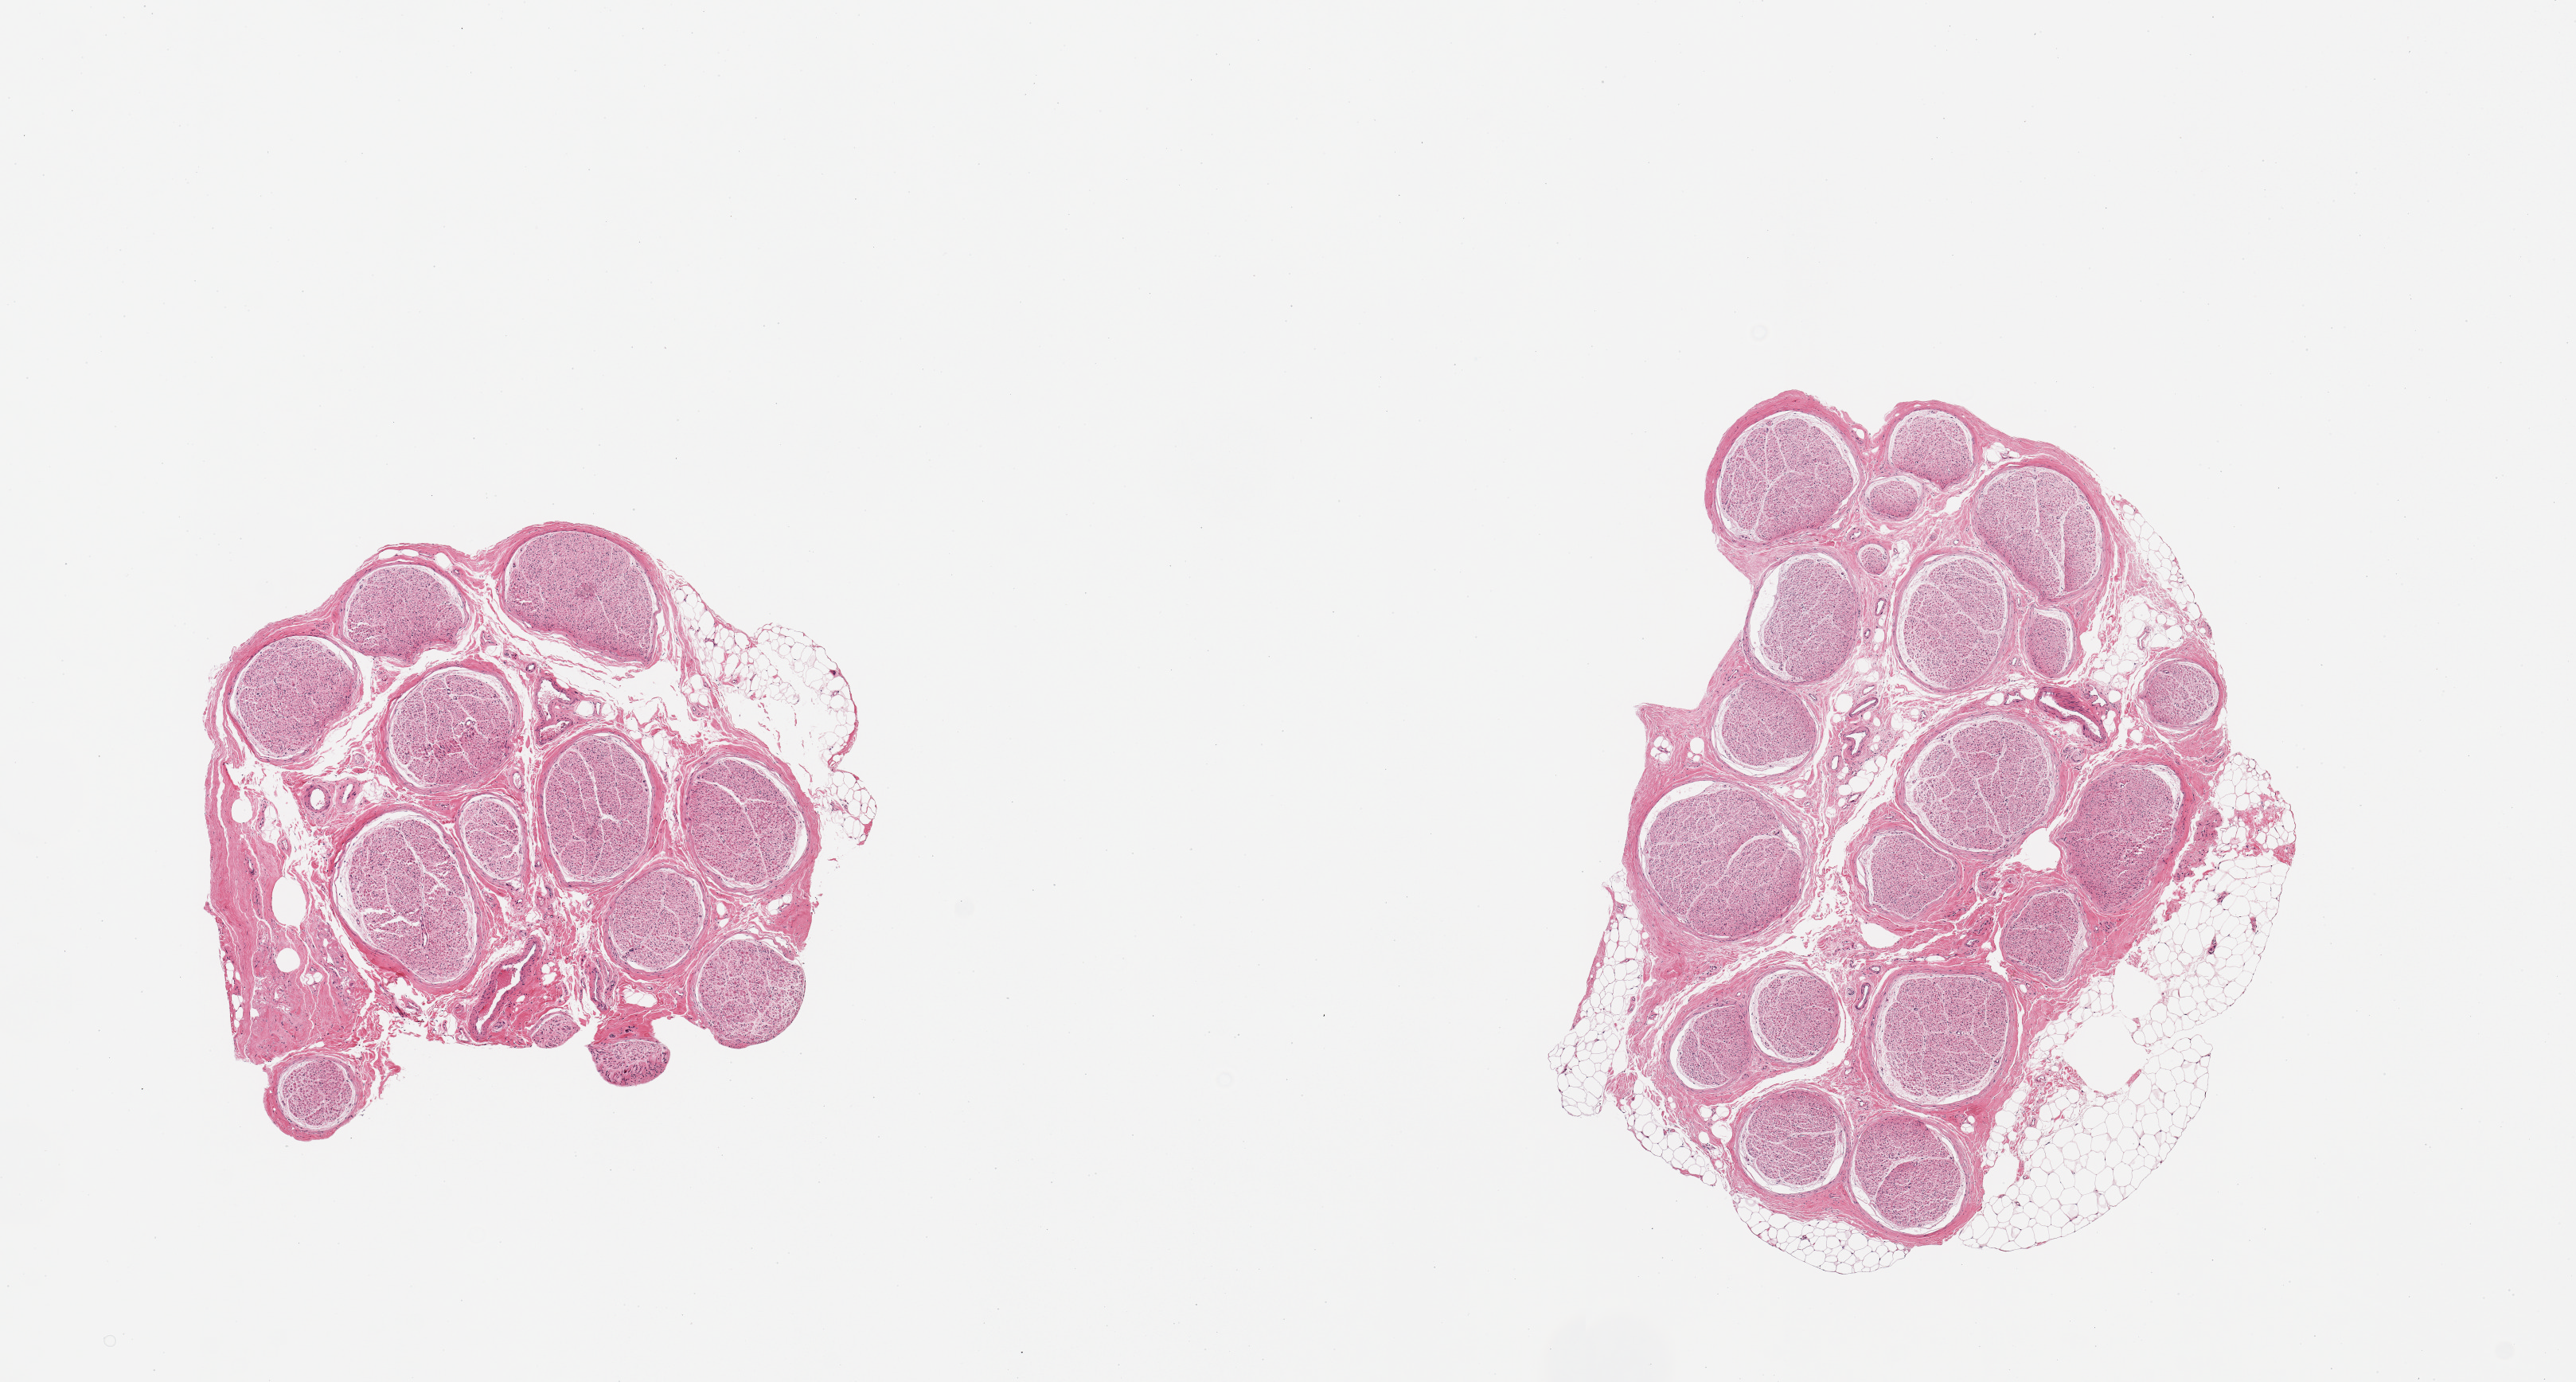
Whole-slide image, hematoxylin and eosin (H&E) stain — low-resolution overview of the scanned area, about 12.8 x 6.9 mm; PAXgene-fixed, paraffin-embedded tissue; section of tibial nerve (target tissue); donor tissue sample. Donor: female.
Pathologist's review note for this sample: 2 pieces; rim of adherent fat ~0.6 to 0.8mm.